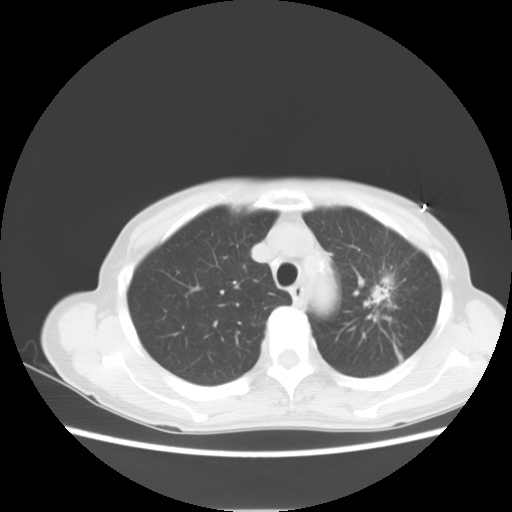
Chest CT, one axial slice; position 7 of 14 along the scan axis; reconstruction kernel STANDARD; 120 kVp; lung window (W 1500 / L -600 HU); 5 mm slice thickness; 512 × 512 image matrix, field of view 350 × 350 mm. Patient: female, 71 years. Case-level facts recorded for this patient, not image findings: clinical TNM (as recorded): T2 N0 M0.
Outlined on this slice (bounding box drawn by a radiologist):
- lung tumour (recorded histology: adenocarcinoma): bounding box (x1, y1, x2, y2) in pixels: (369, 282, 391, 306)